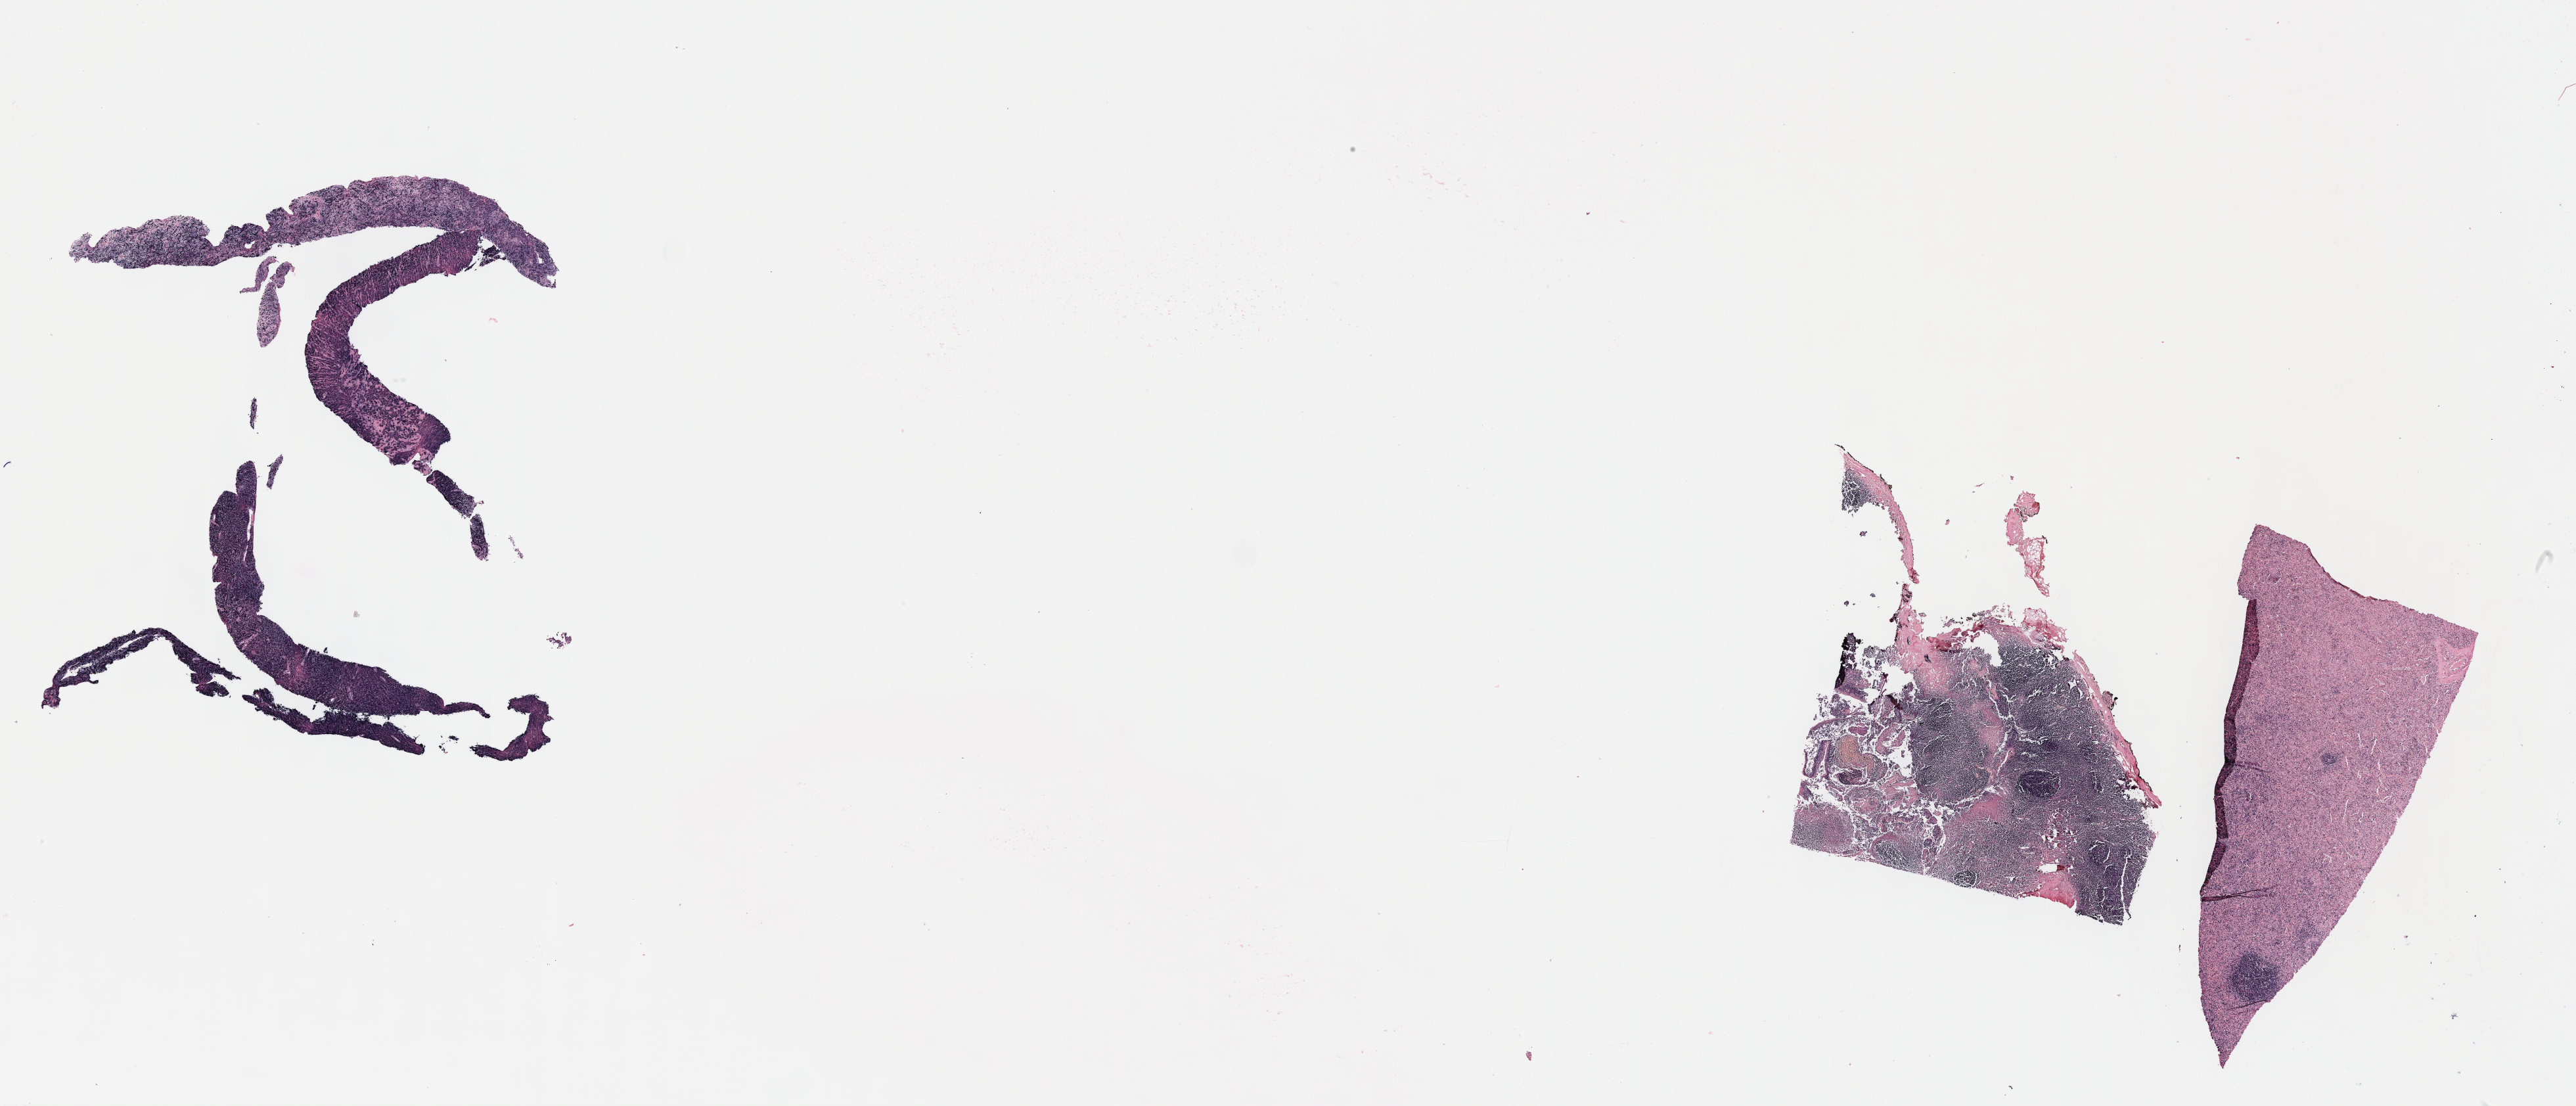
Whole-slide image; stain recorded as Iodonitrotetrazolium, a low-resolution overview of the entire scanned area, about 31.7 x 13.6 mm; specimen: tumor tissue; site: pleura. Patient: male, age at initial diagnosis 2 years.
- histologic diagnosis: Diffuse large B-cell lymphoma, NOS